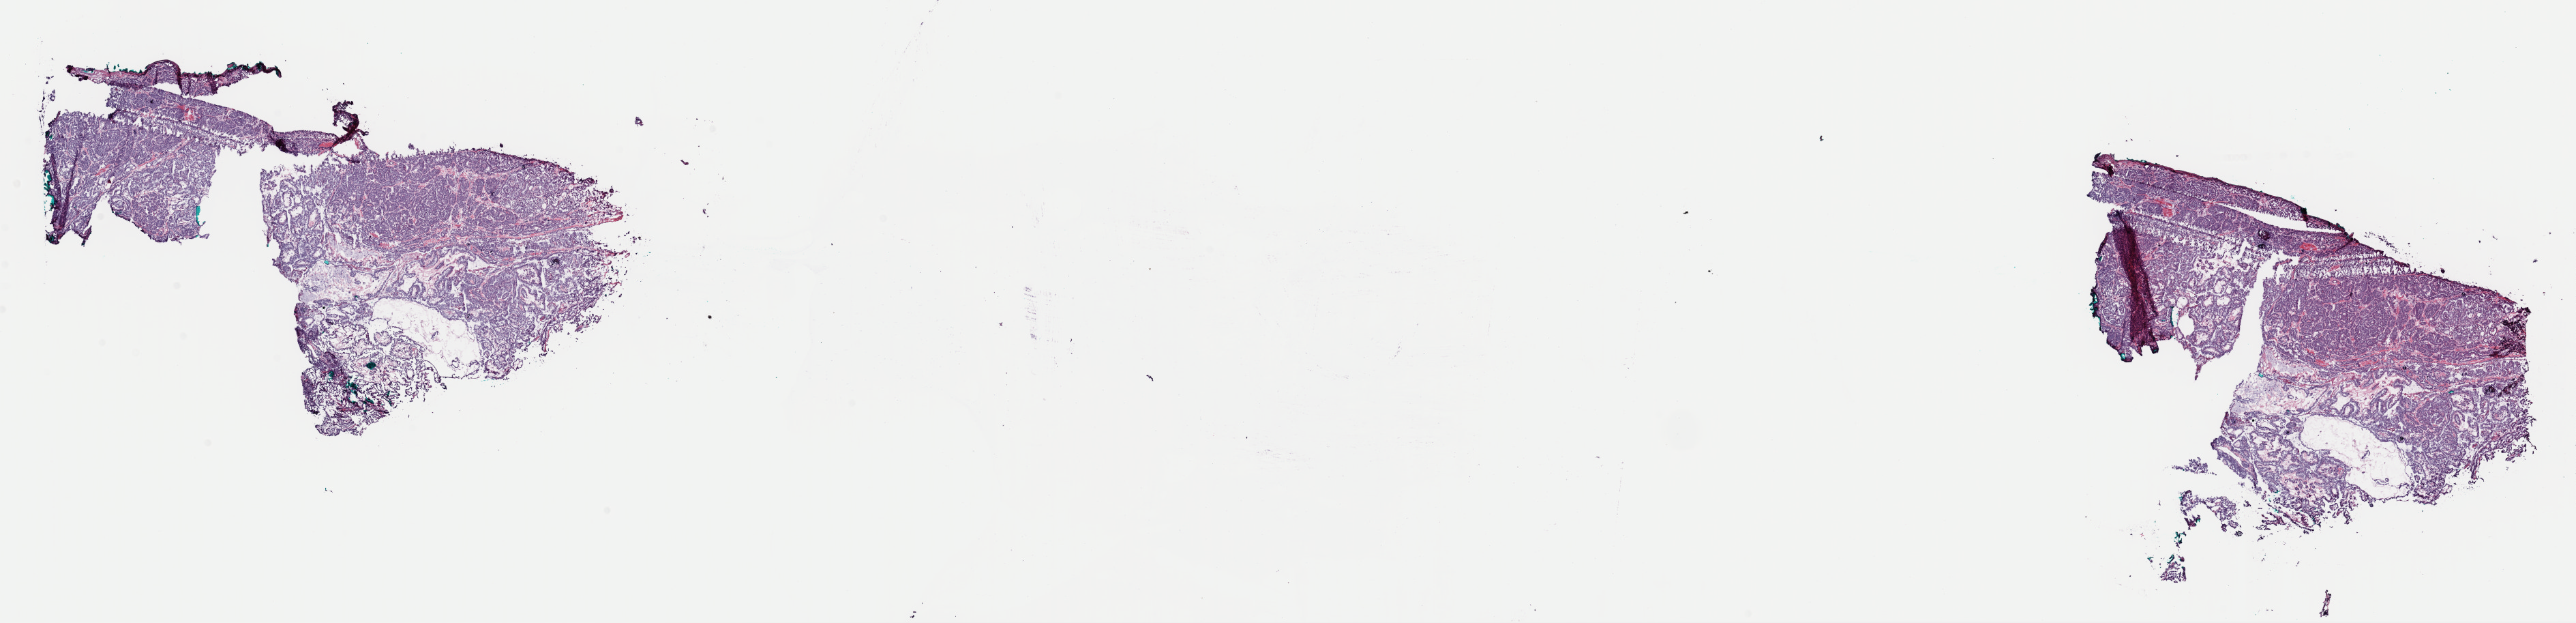
Hematoxylin and eosin (H&E) stained whole-slide image, whole scanned area (about 29.8 x 7.2 mm) shown as a low-resolution overview. Frozen section. Sample: primary tumour, thyroid. Female patient; age at initial diagnosis 58 years. Slide review estimates, as recorded: tumour cells 100%, tumour nuclei 90%, normal cells 0%, stromal cells 0%, necrosis 0%. Inflammatory infiltration, as recorded: lymphocyte infiltration 0%, monocyte infiltration 0%, neutrophil infiltration 0%.
- pathologic diagnosis: Papillary adenocarcinoma, NOS
- AJCC pathologic stage: III (7th edition)
- TNM: T3 N0 M0